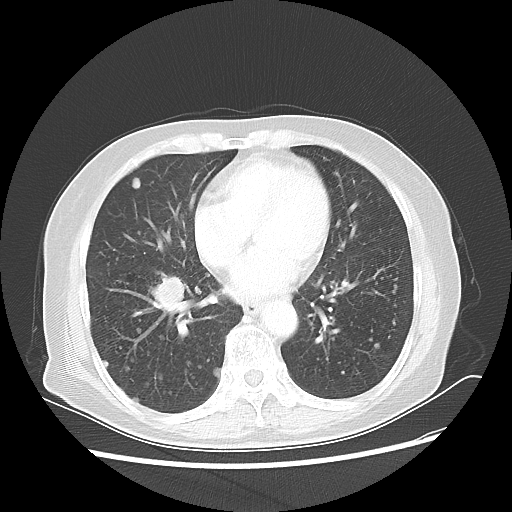
Chest CT, one axial slice. Position 22 of 56 along the scan axis. Reconstruction kernel LUNG. 80 kVp. Lung window (W 1500 / L -600 HU). 5 mm slice thickness. 512 × 512 image matrix, field of view 360 × 360 mm. Patient: female, 68 years. From the clinical record (not read from this slice): clinical TNM (as recorded): T1c N3 M0.
Structures marked on this image (bounding box drawn by a radiologist):
- lung tumour (recorded histology: squamous cell carcinoma): box from (x=142, y=276) to (x=192, y=325) px